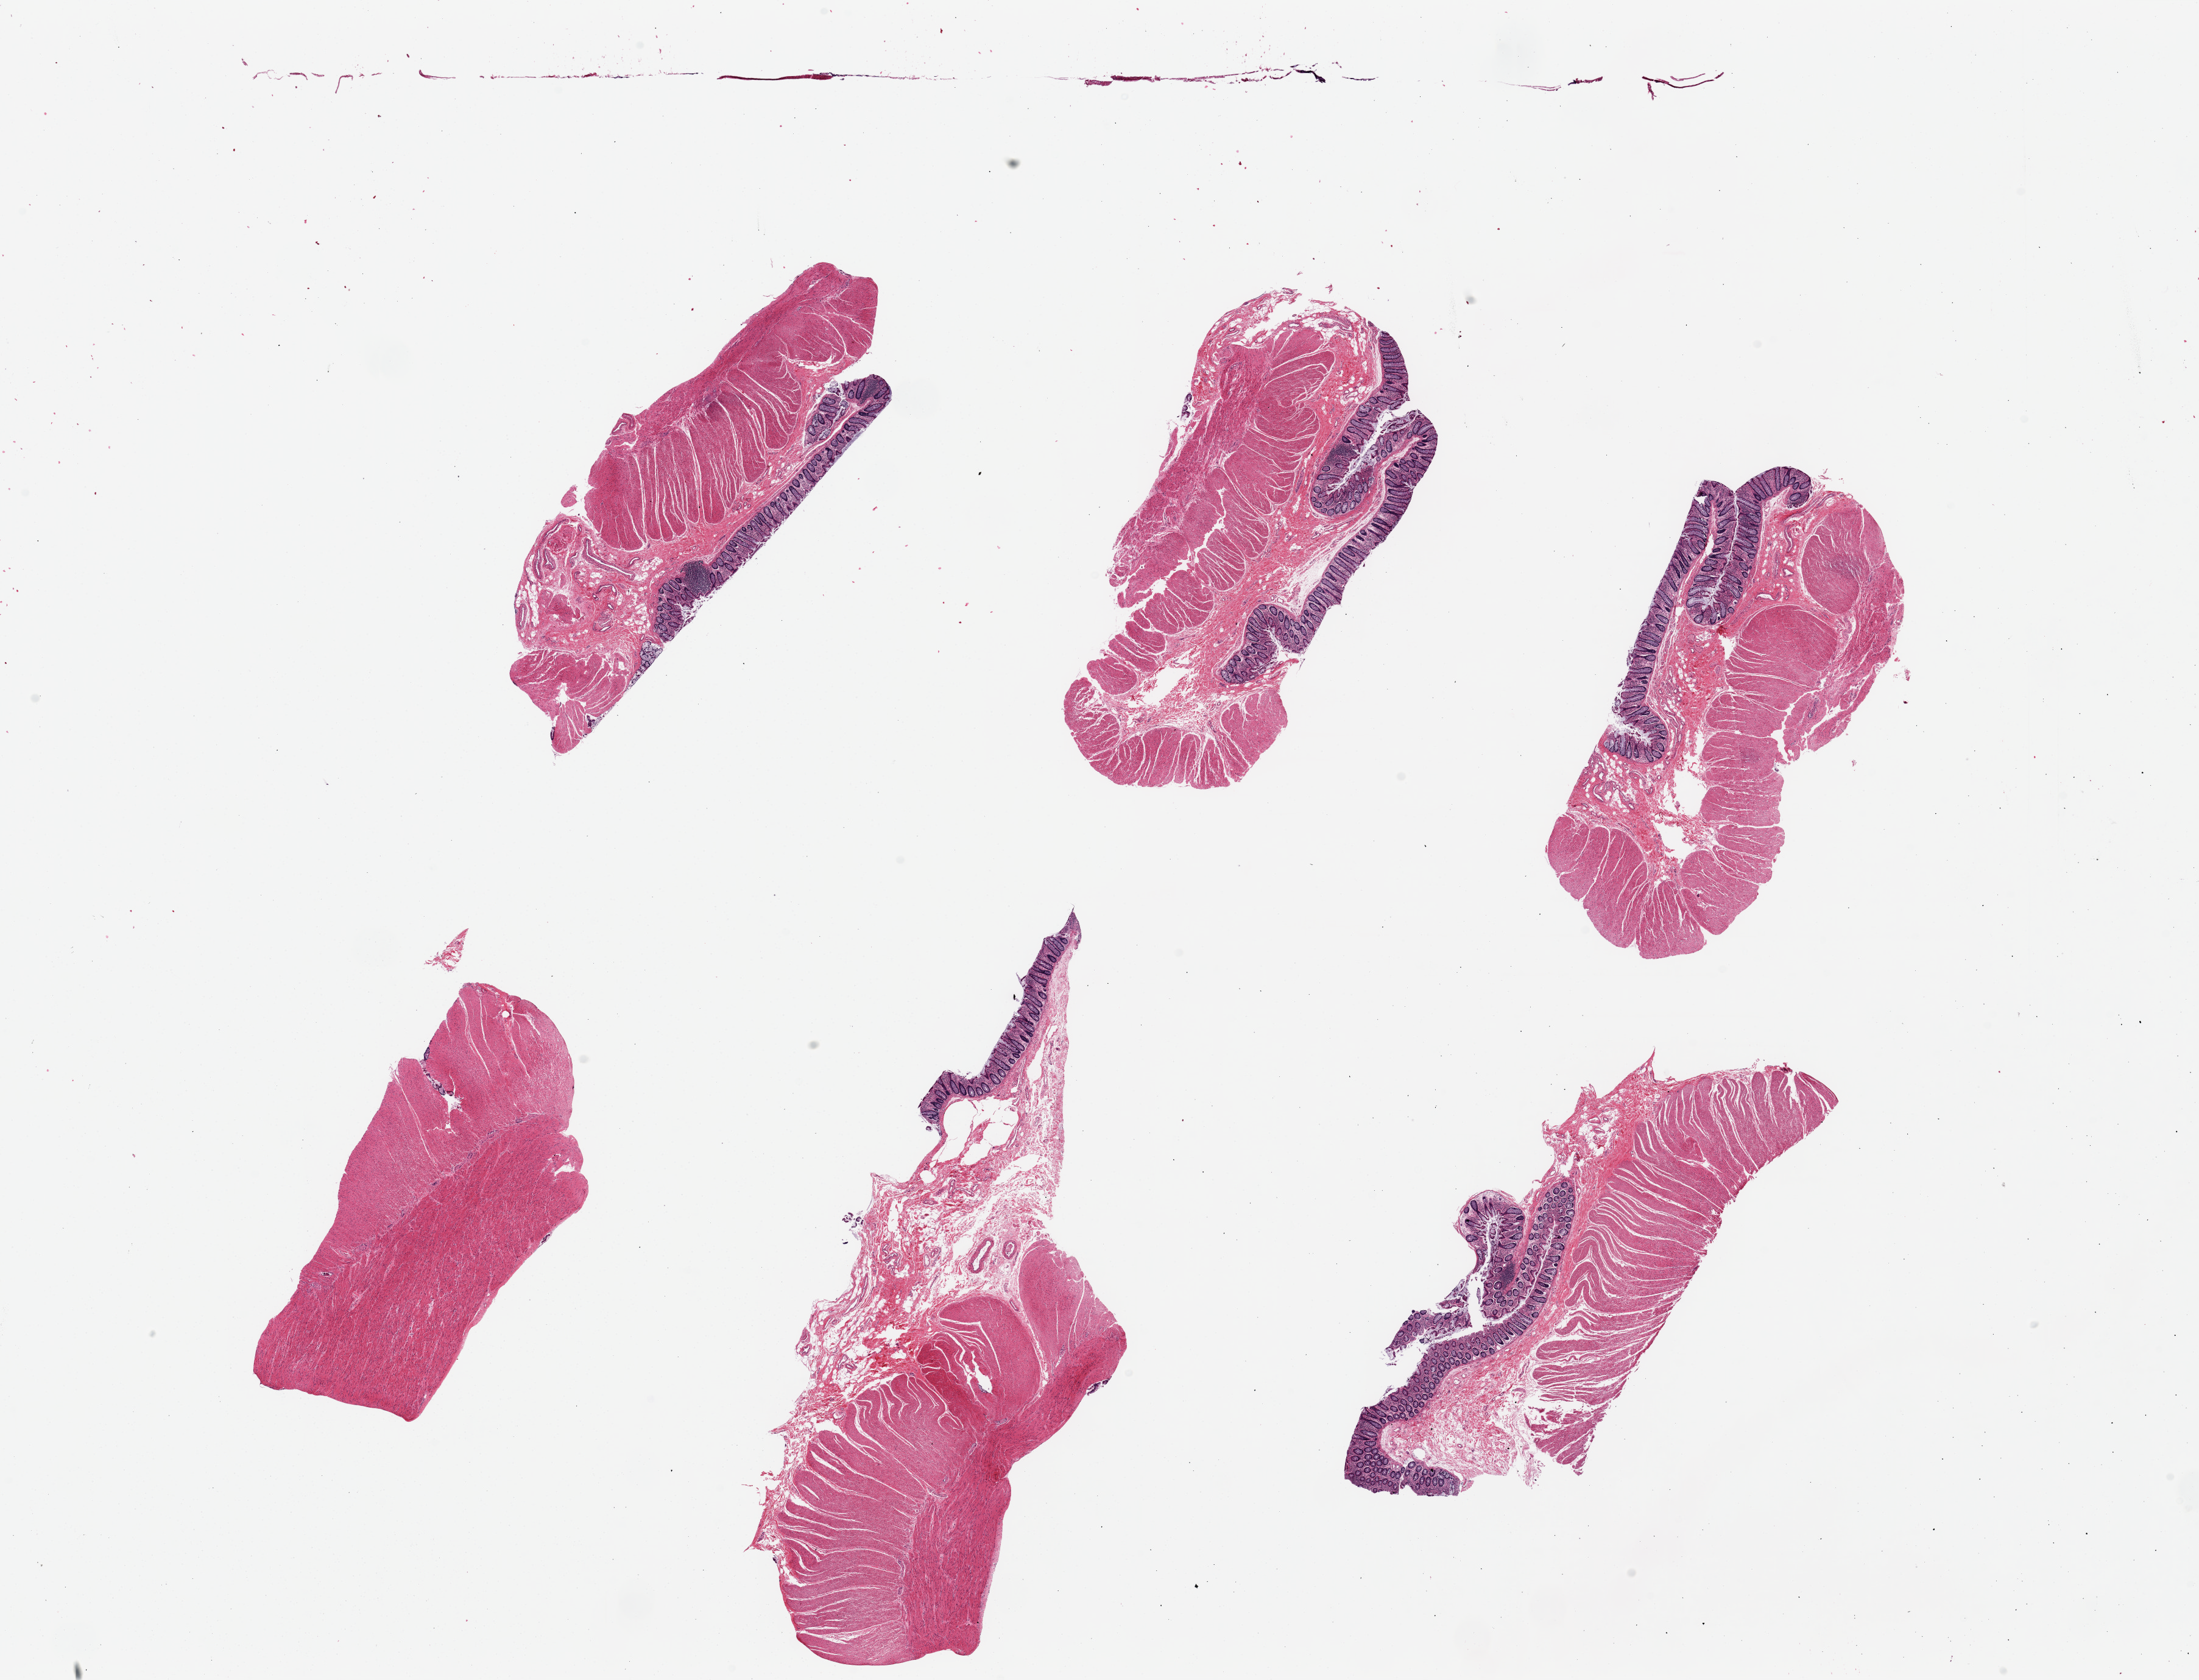
Digitized haematoxylin and eosin-stained section, a low-resolution overview of the entire scanned area, about 28.5 x 21.8 mm. PAXgene-fixed, paraffin-embedded tissue. Section of sigmoid colon (target tissue). Donor tissue sample. Male donor.
Reviewer comment on this tissue sample: 6 pieces, up to 10x4mm; All have muscularis propria (our target) but 5 of 6 have (unwanted) mucosa.